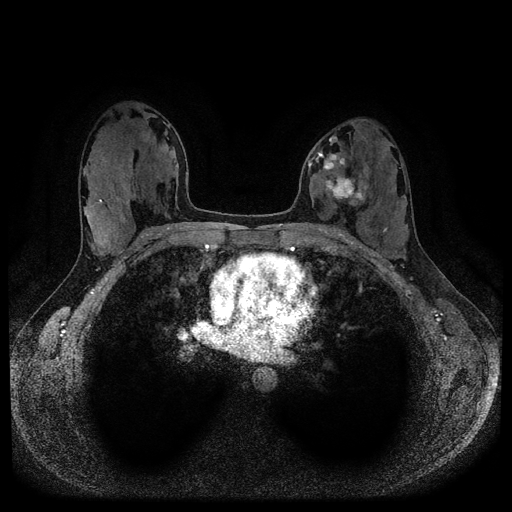
Breast MRI (dynamic contrast-enhanced, multi-phase), one axial slice. Slice 57 of 116 in the series (ordered by position). Dynamic contrast-enhanced series, time point 2 of 5 at this slice position (early post-contrast). 1.5 T. TE 2.6 ms, TR 5.3 ms. 2 mm slice thickness. 512 × 512 image matrix. Female patient, age 33 years.
Outlined on this slice (semi-automatic segmentation, software-assisted and operator-edited):
- breast lesion (labelled 'tumour' in the annotation; benign lesions carry a separate 'benign' label): bounding box [x1, y1, x2, y2] px = [323, 152, 365, 205]